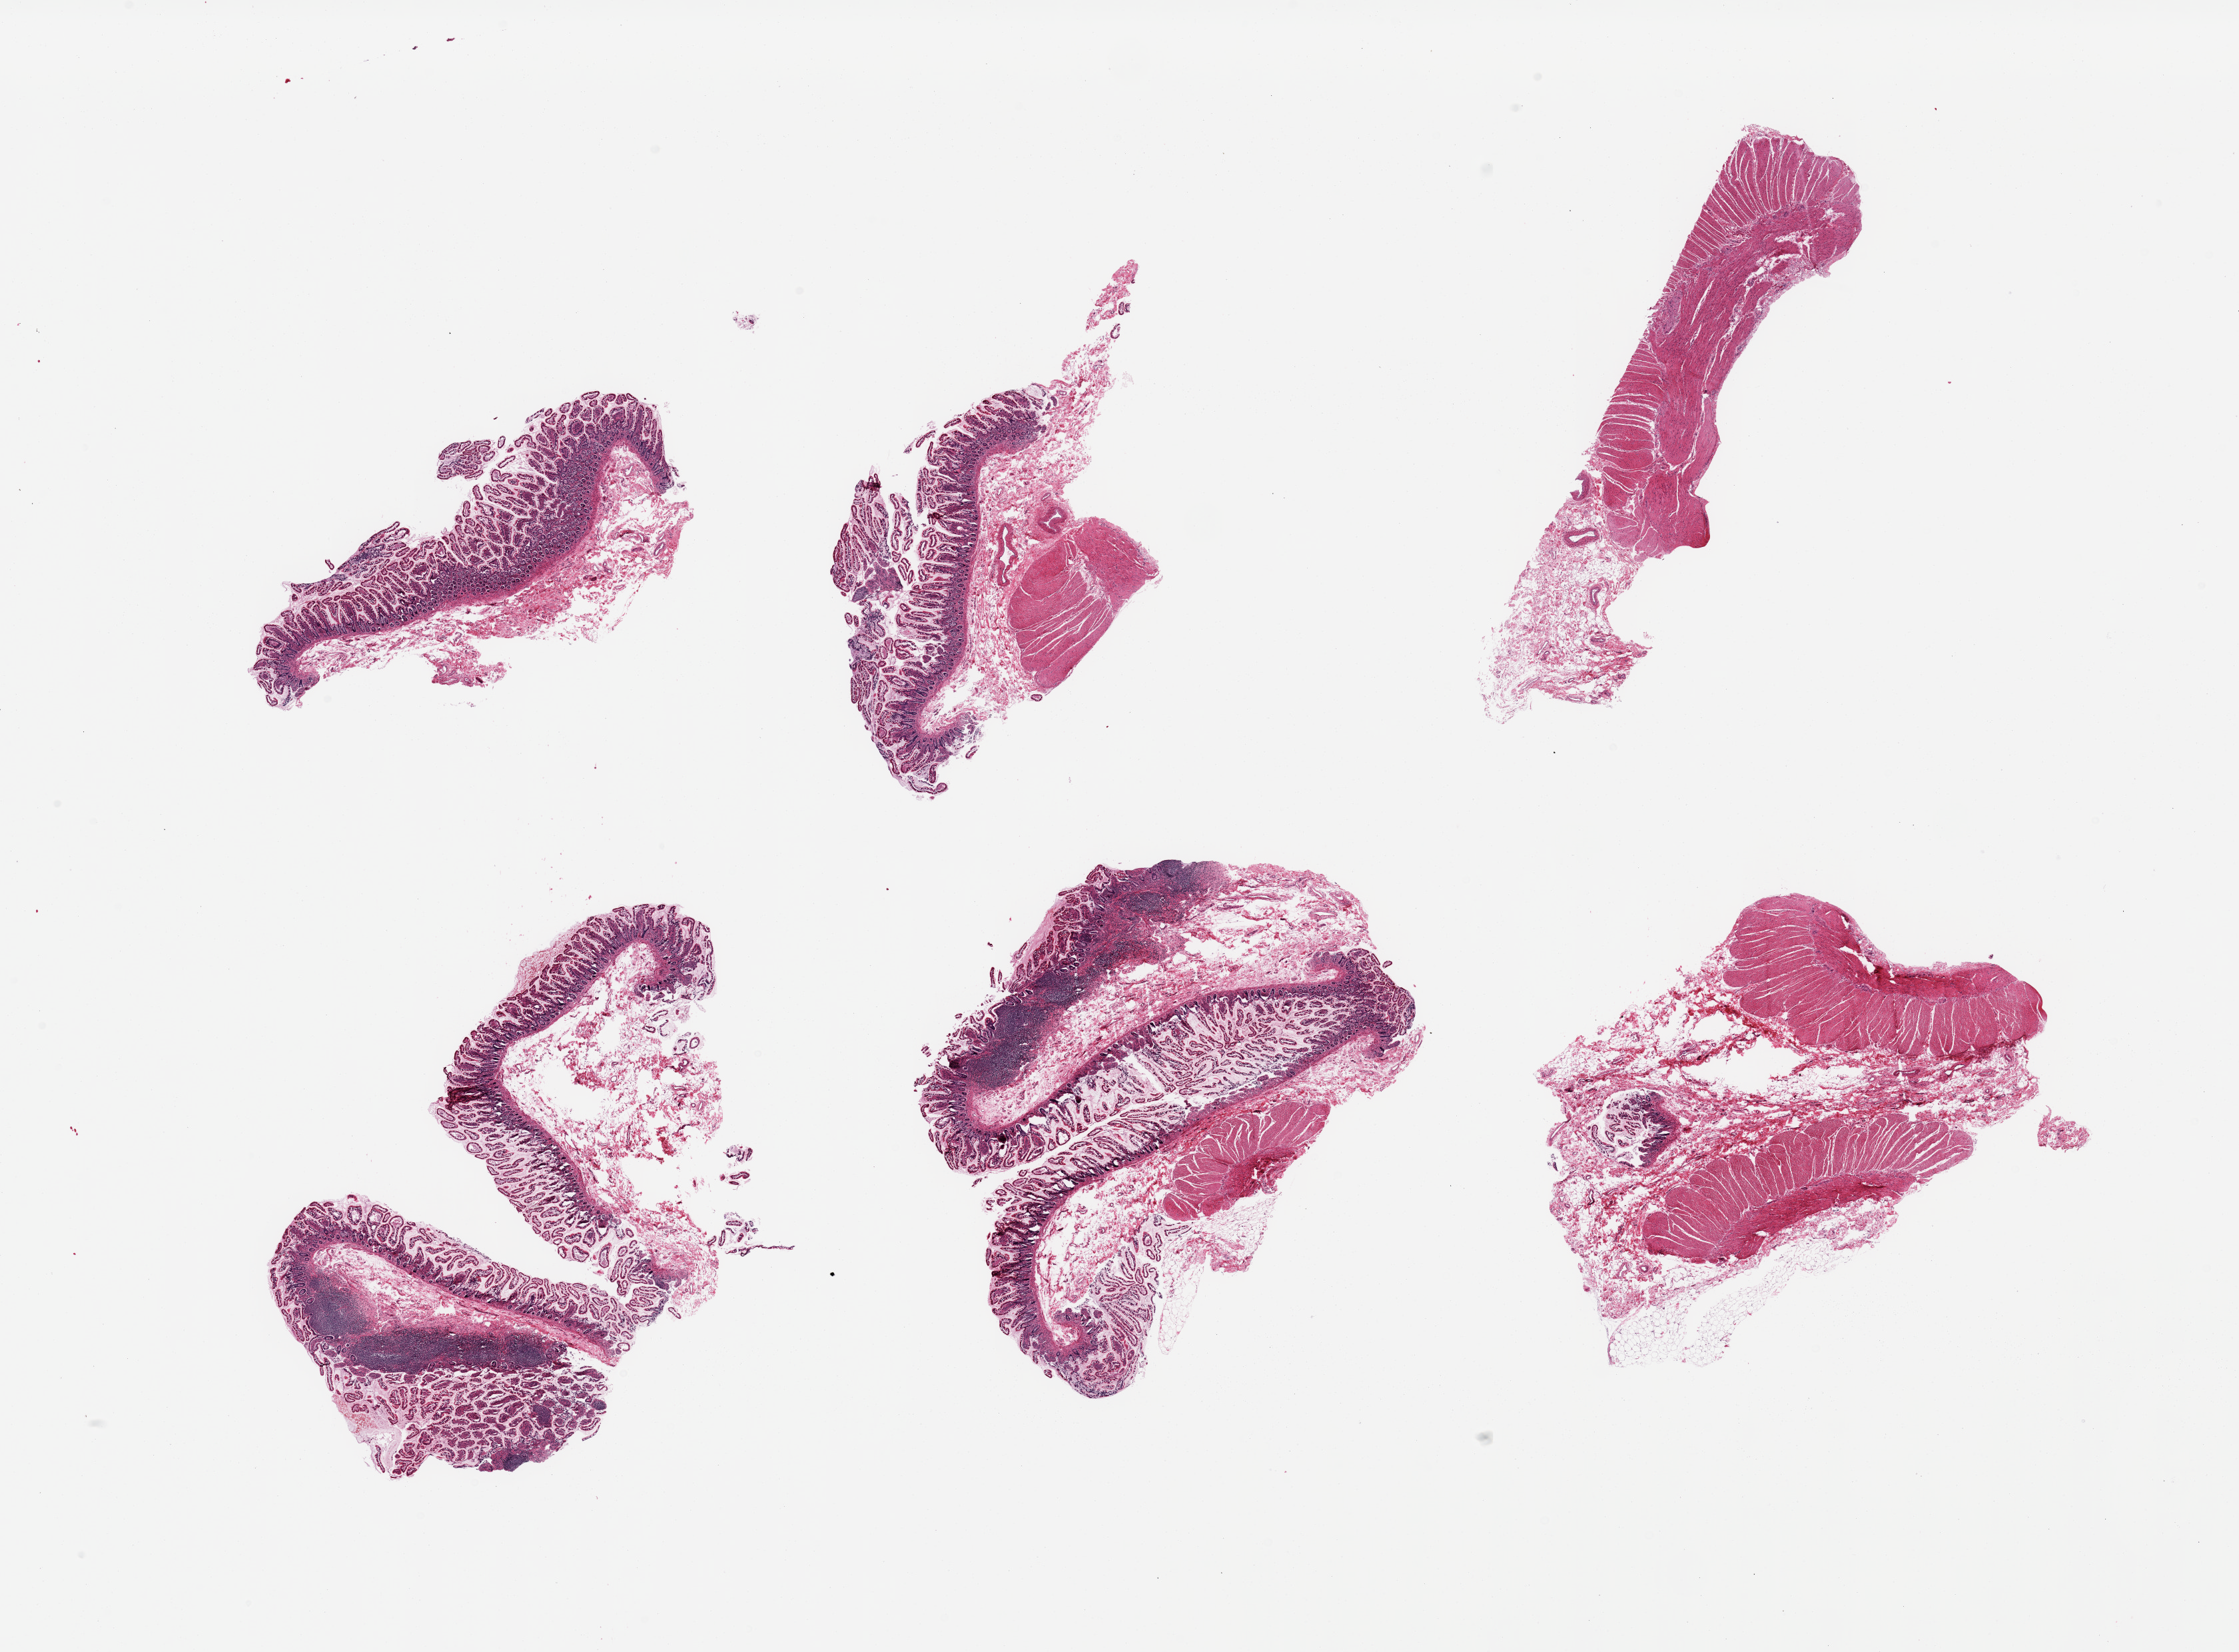
Whole-slide image, H&E stain, shown as a low-resolution overview of the whole scanned area (about 26.6 x 19.6 mm), PAXgene-fixed paraffin-embedded (PFPE) section, sampled site (target tissue): sigmoid colon, tissue donor sample.
Pathologist's review note for this sample: 6 pieces, small bowel, fat, and muscularis, no sigmoid colon muscularis.